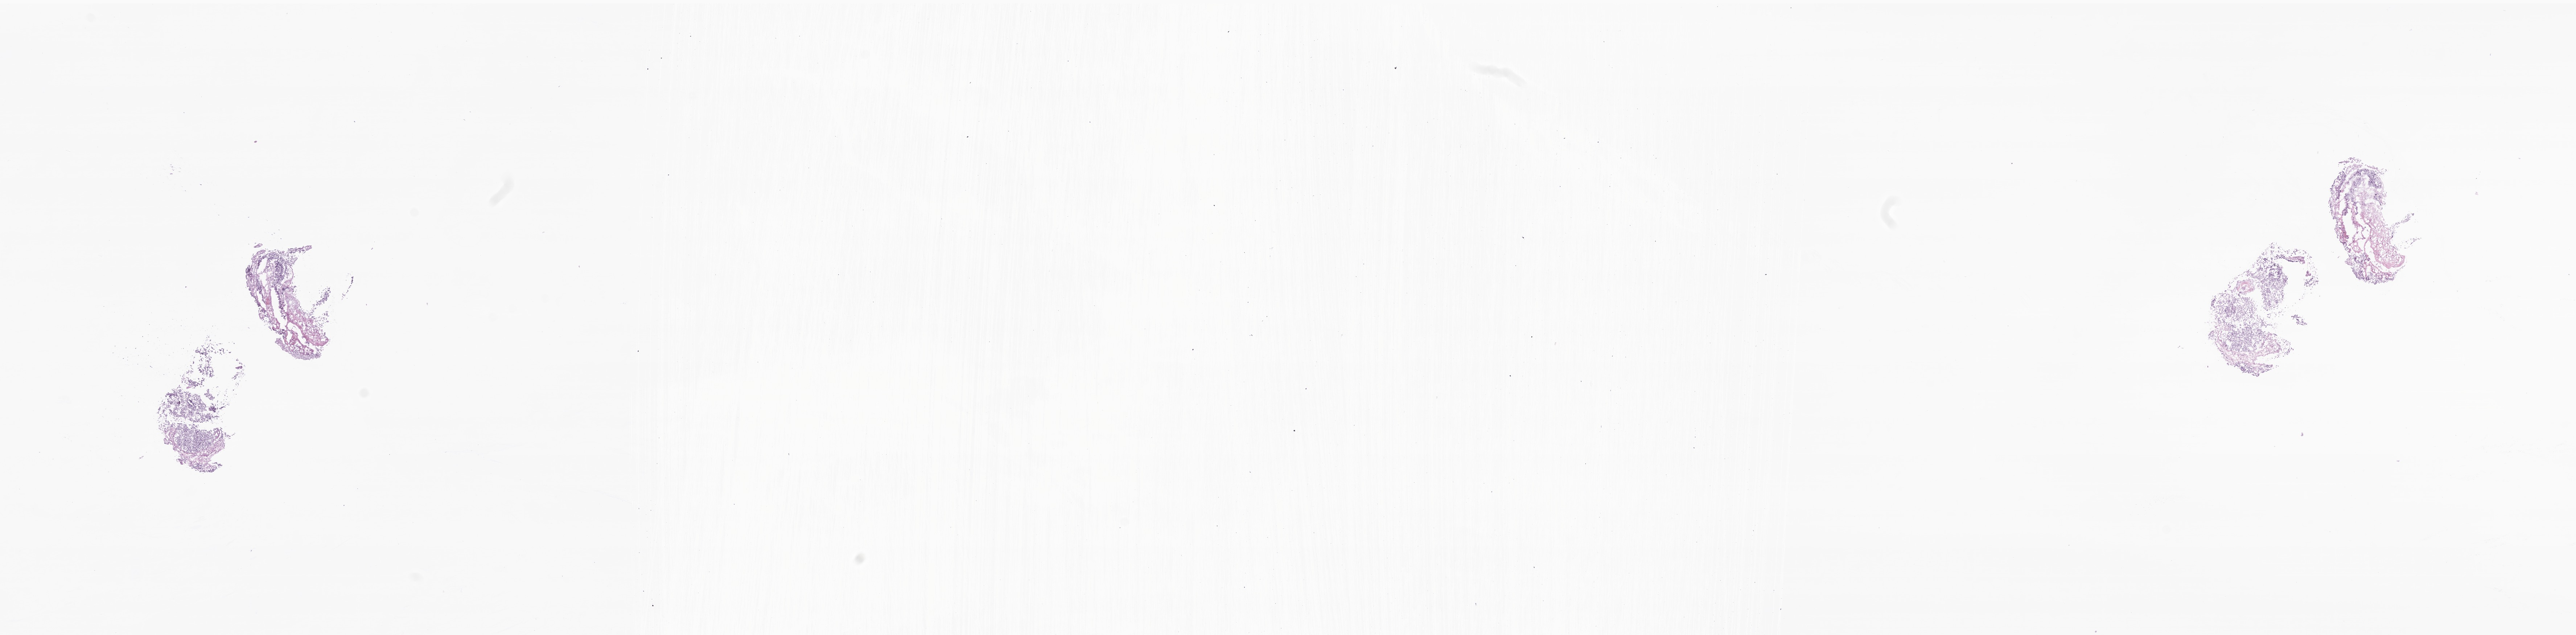
Digitized hematoxylin and eosin (H&E)-stained section of tumor tissue from the brain — shown as a low-resolution overview of the whole scanned area (about 29.9 x 7.4 mm). Frozen section. Patient female; age 37 months (3 years 1 month).
Recorded diagnosis: CNS embryonal tumor, NOS.